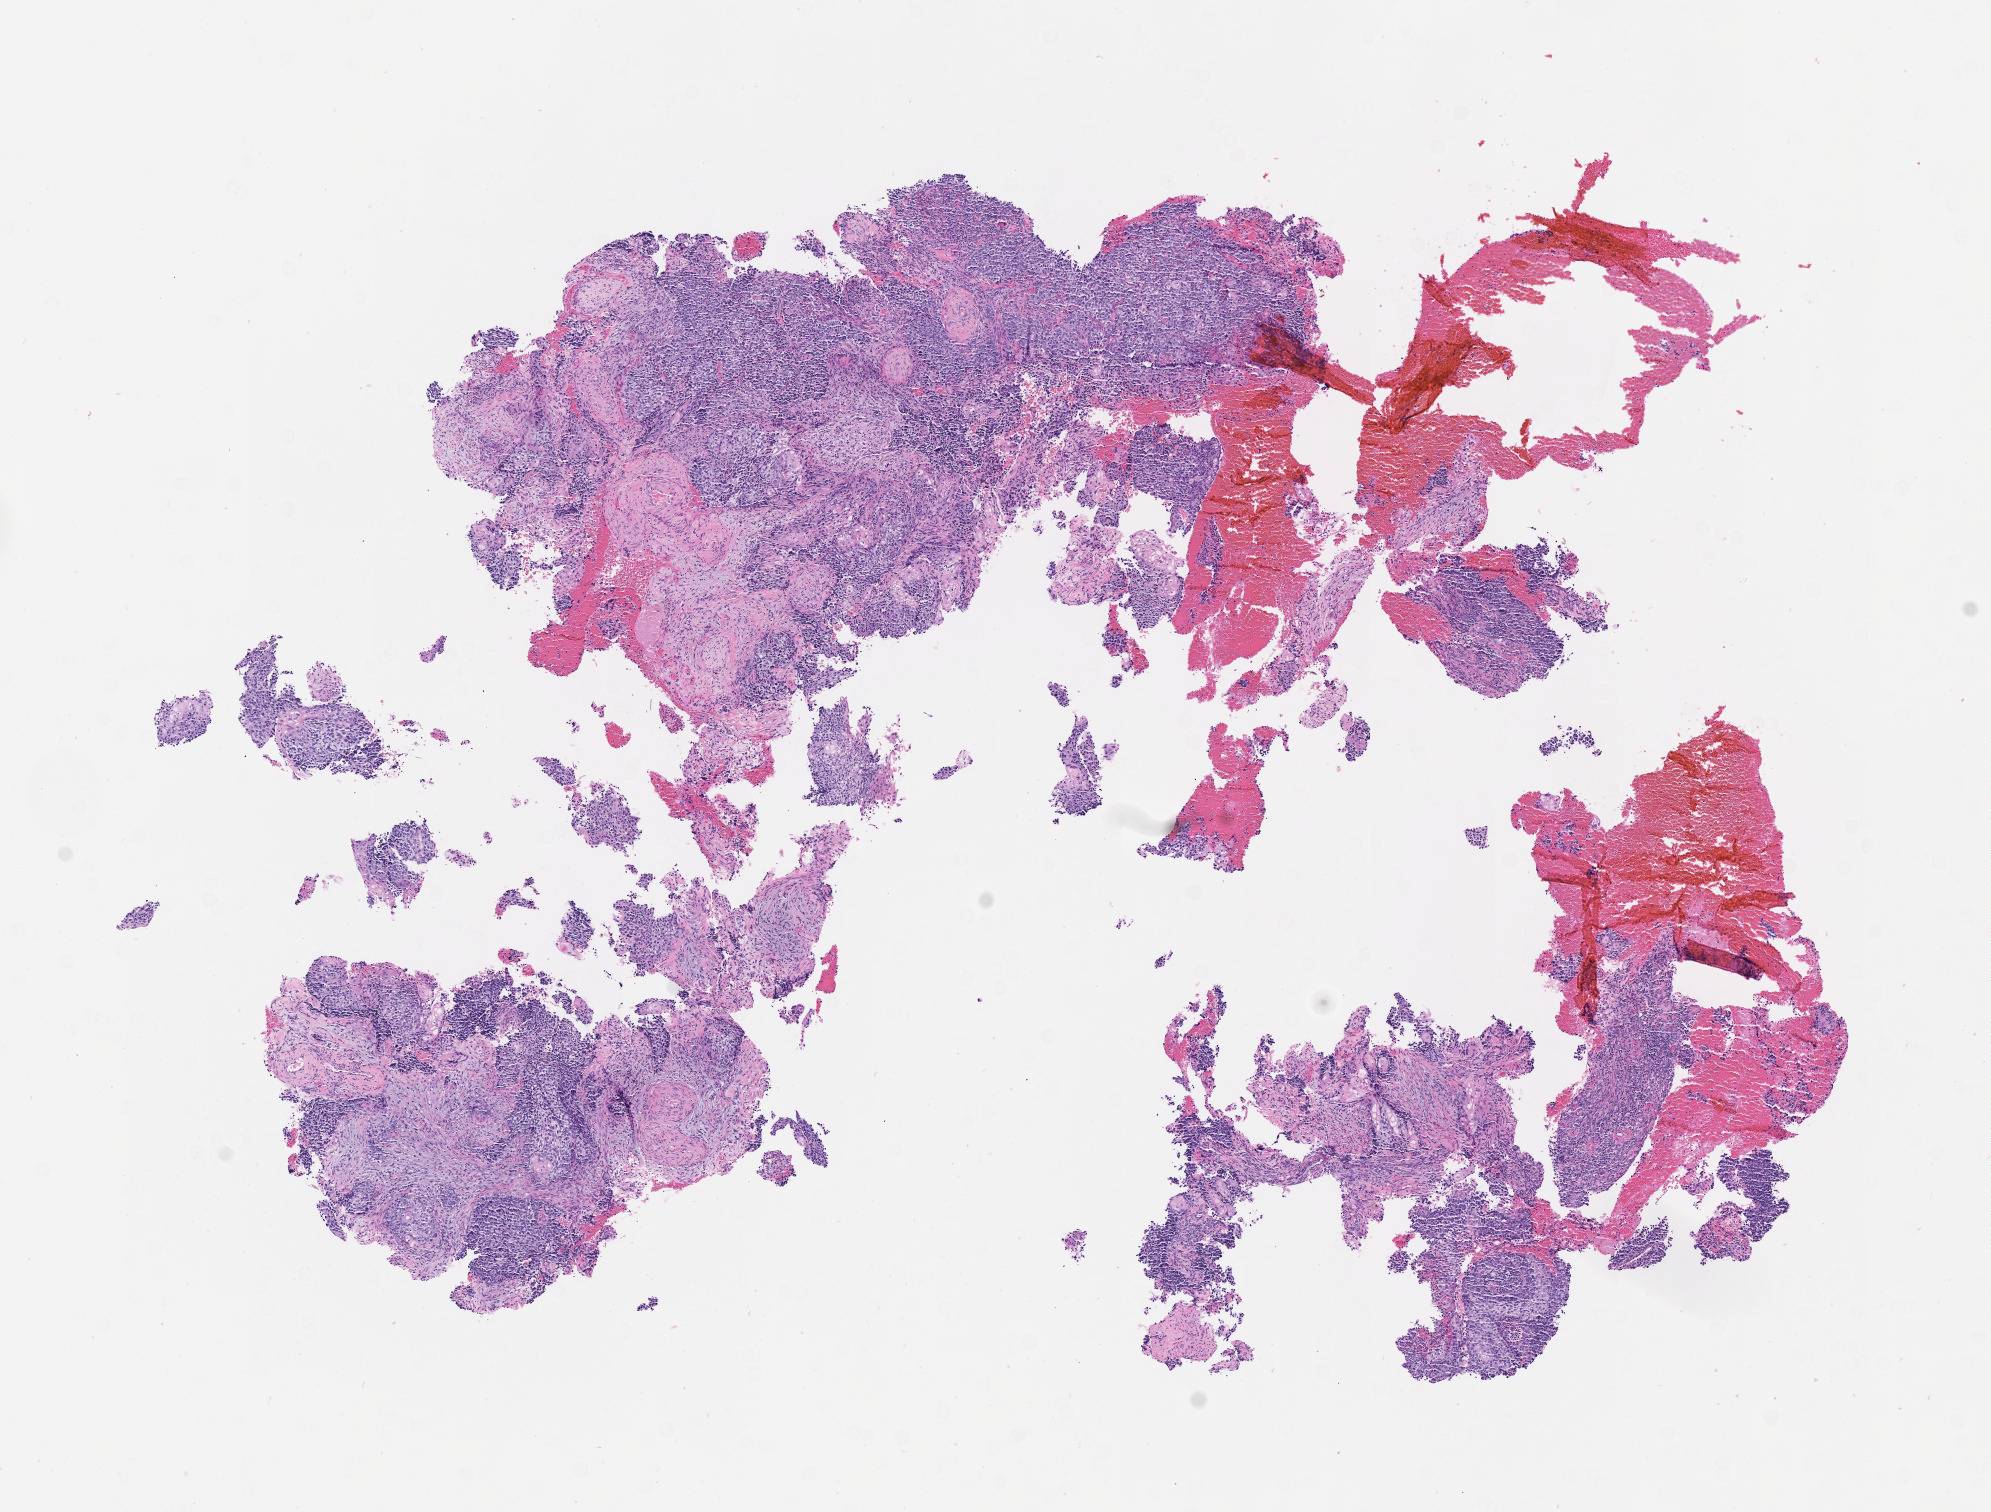
Whole-slide image, haematoxylin and eosin stain, shown as a low-resolution overview of the whole scanned area (about 8.1 x 6.1 mm). Tumor tissue. Site: cervix. Female patient, age 58 years.
Histologic diagnosis: Squamous cell carcinoma, large cell, nonkeratinizing, NOS.